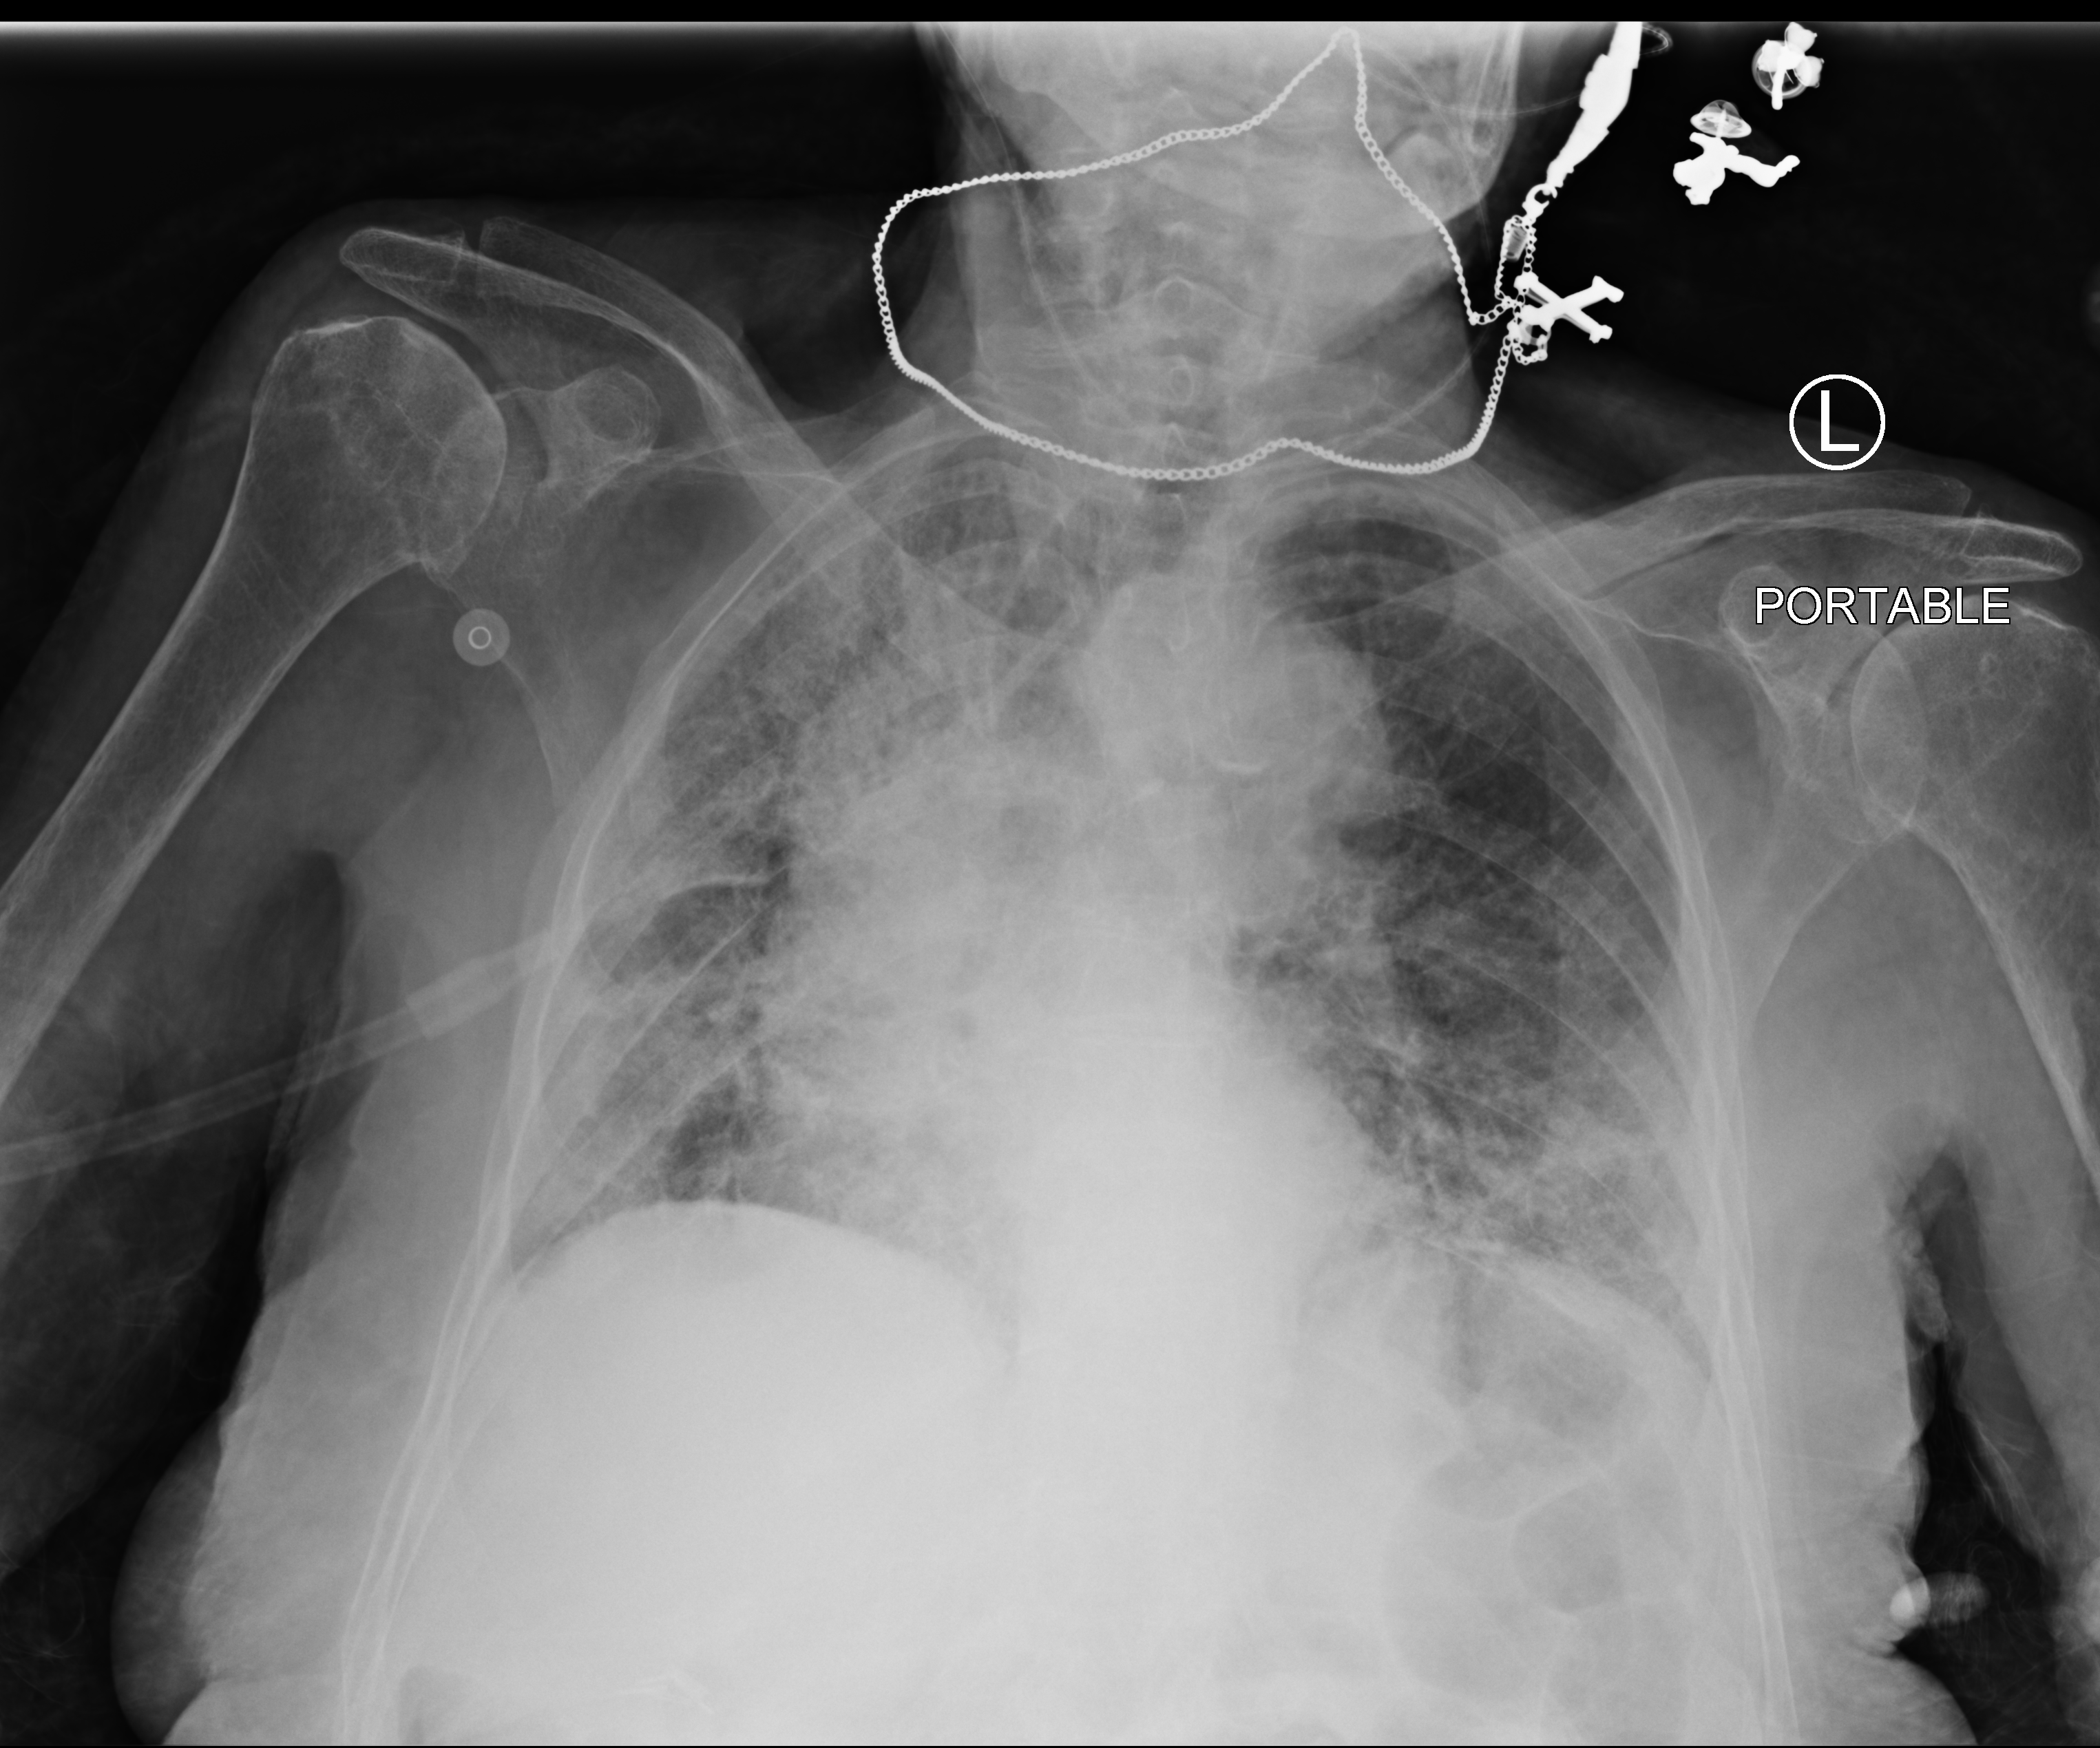
Portable chest radiograph. Patient hospitalised with COVID-19; female, aged 75–90 years.
Hospital-stay facts (about this admission, not read from this image; timing relative to this image not recorded): mechanically ventilated during this hospital stay: no.